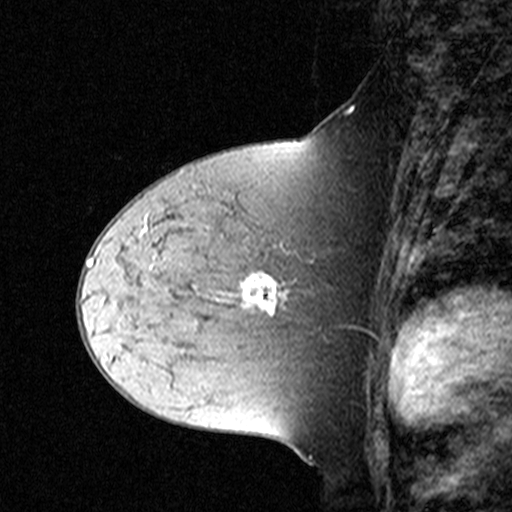
Breast MRI (dynamic contrast-enhanced), one sagittal slice. Position 20 of 44 along the scan axis. Dynamic contrast-enhanced study with each time point stored as its own series, time point 2 of 3 at this slice position (early post-contrast, ordered by acquisition time). 1.5 T. TE 4.5 ms, TR 11 ms. 3 mm slice thickness. 512 × 512 image matrix, field of view 200 × 200 mm. Female patient, age 44 years. Case-level facts recorded for this patient, not image findings: setting: breast cancer imaged before/during neoadjuvant chemotherapy; receptor status: triple-negative.
Annotated regions visible in this slice (semi-automatic segmentation, software-assisted and operator-edited):
- analysis volume of interest (the breast-tissue region the enhancement analysis was run in; not a lesion): bounding box <132,212,309,331> (left, top, right, bottom; pixels)
- tumour enhancement mask (voxels above the 90 % enhancement threshold inside the analysis volume of interest): <243,272,278,312>